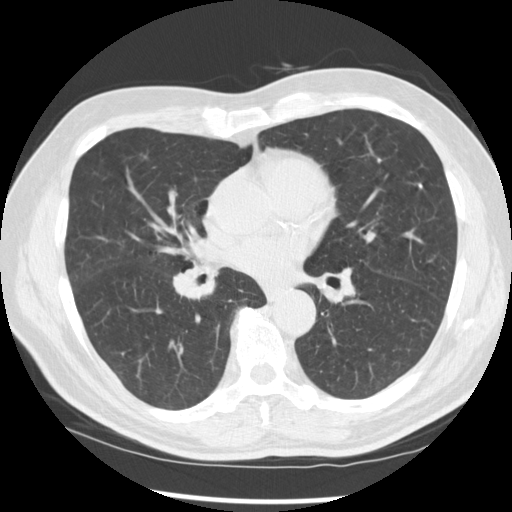
Low-dose screening chest CT, one axial slice; position 142 of 277 along the scan axis; 120 kVp; lung window (W 1500 / L -600 HU); 512 × 512 image matrix.
Annotated regions visible in this slice (manually delineated by an expert):
- lesion 1 (tumor, middle lobe of right lung): bounding box <173,264,214,301> (left, top, right, bottom; pixels)